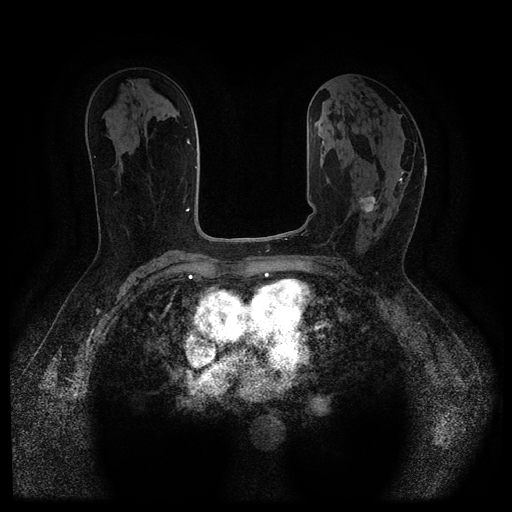
Breast MRI (dynamic contrast-enhanced, multi-phase), one axial slice; slice 57 of 116 in the series (ordered by position); dynamic contrast-enhanced series, time point 2 of 5 at this slice position (early post-contrast); 1.5 T; TE 2.6 ms, TR 5.4 ms; 2 mm slice thickness; 512 × 512 image matrix, field of view 340 × 340 mm. Patient: female, 64 years.
Outlined on this slice (semi-automatically segmented with operator editing):
- breast lesion (labelled 'tumour' in the annotation; benign lesions carry a separate 'benign' label): box from (x=358, y=194) to (x=379, y=215) px